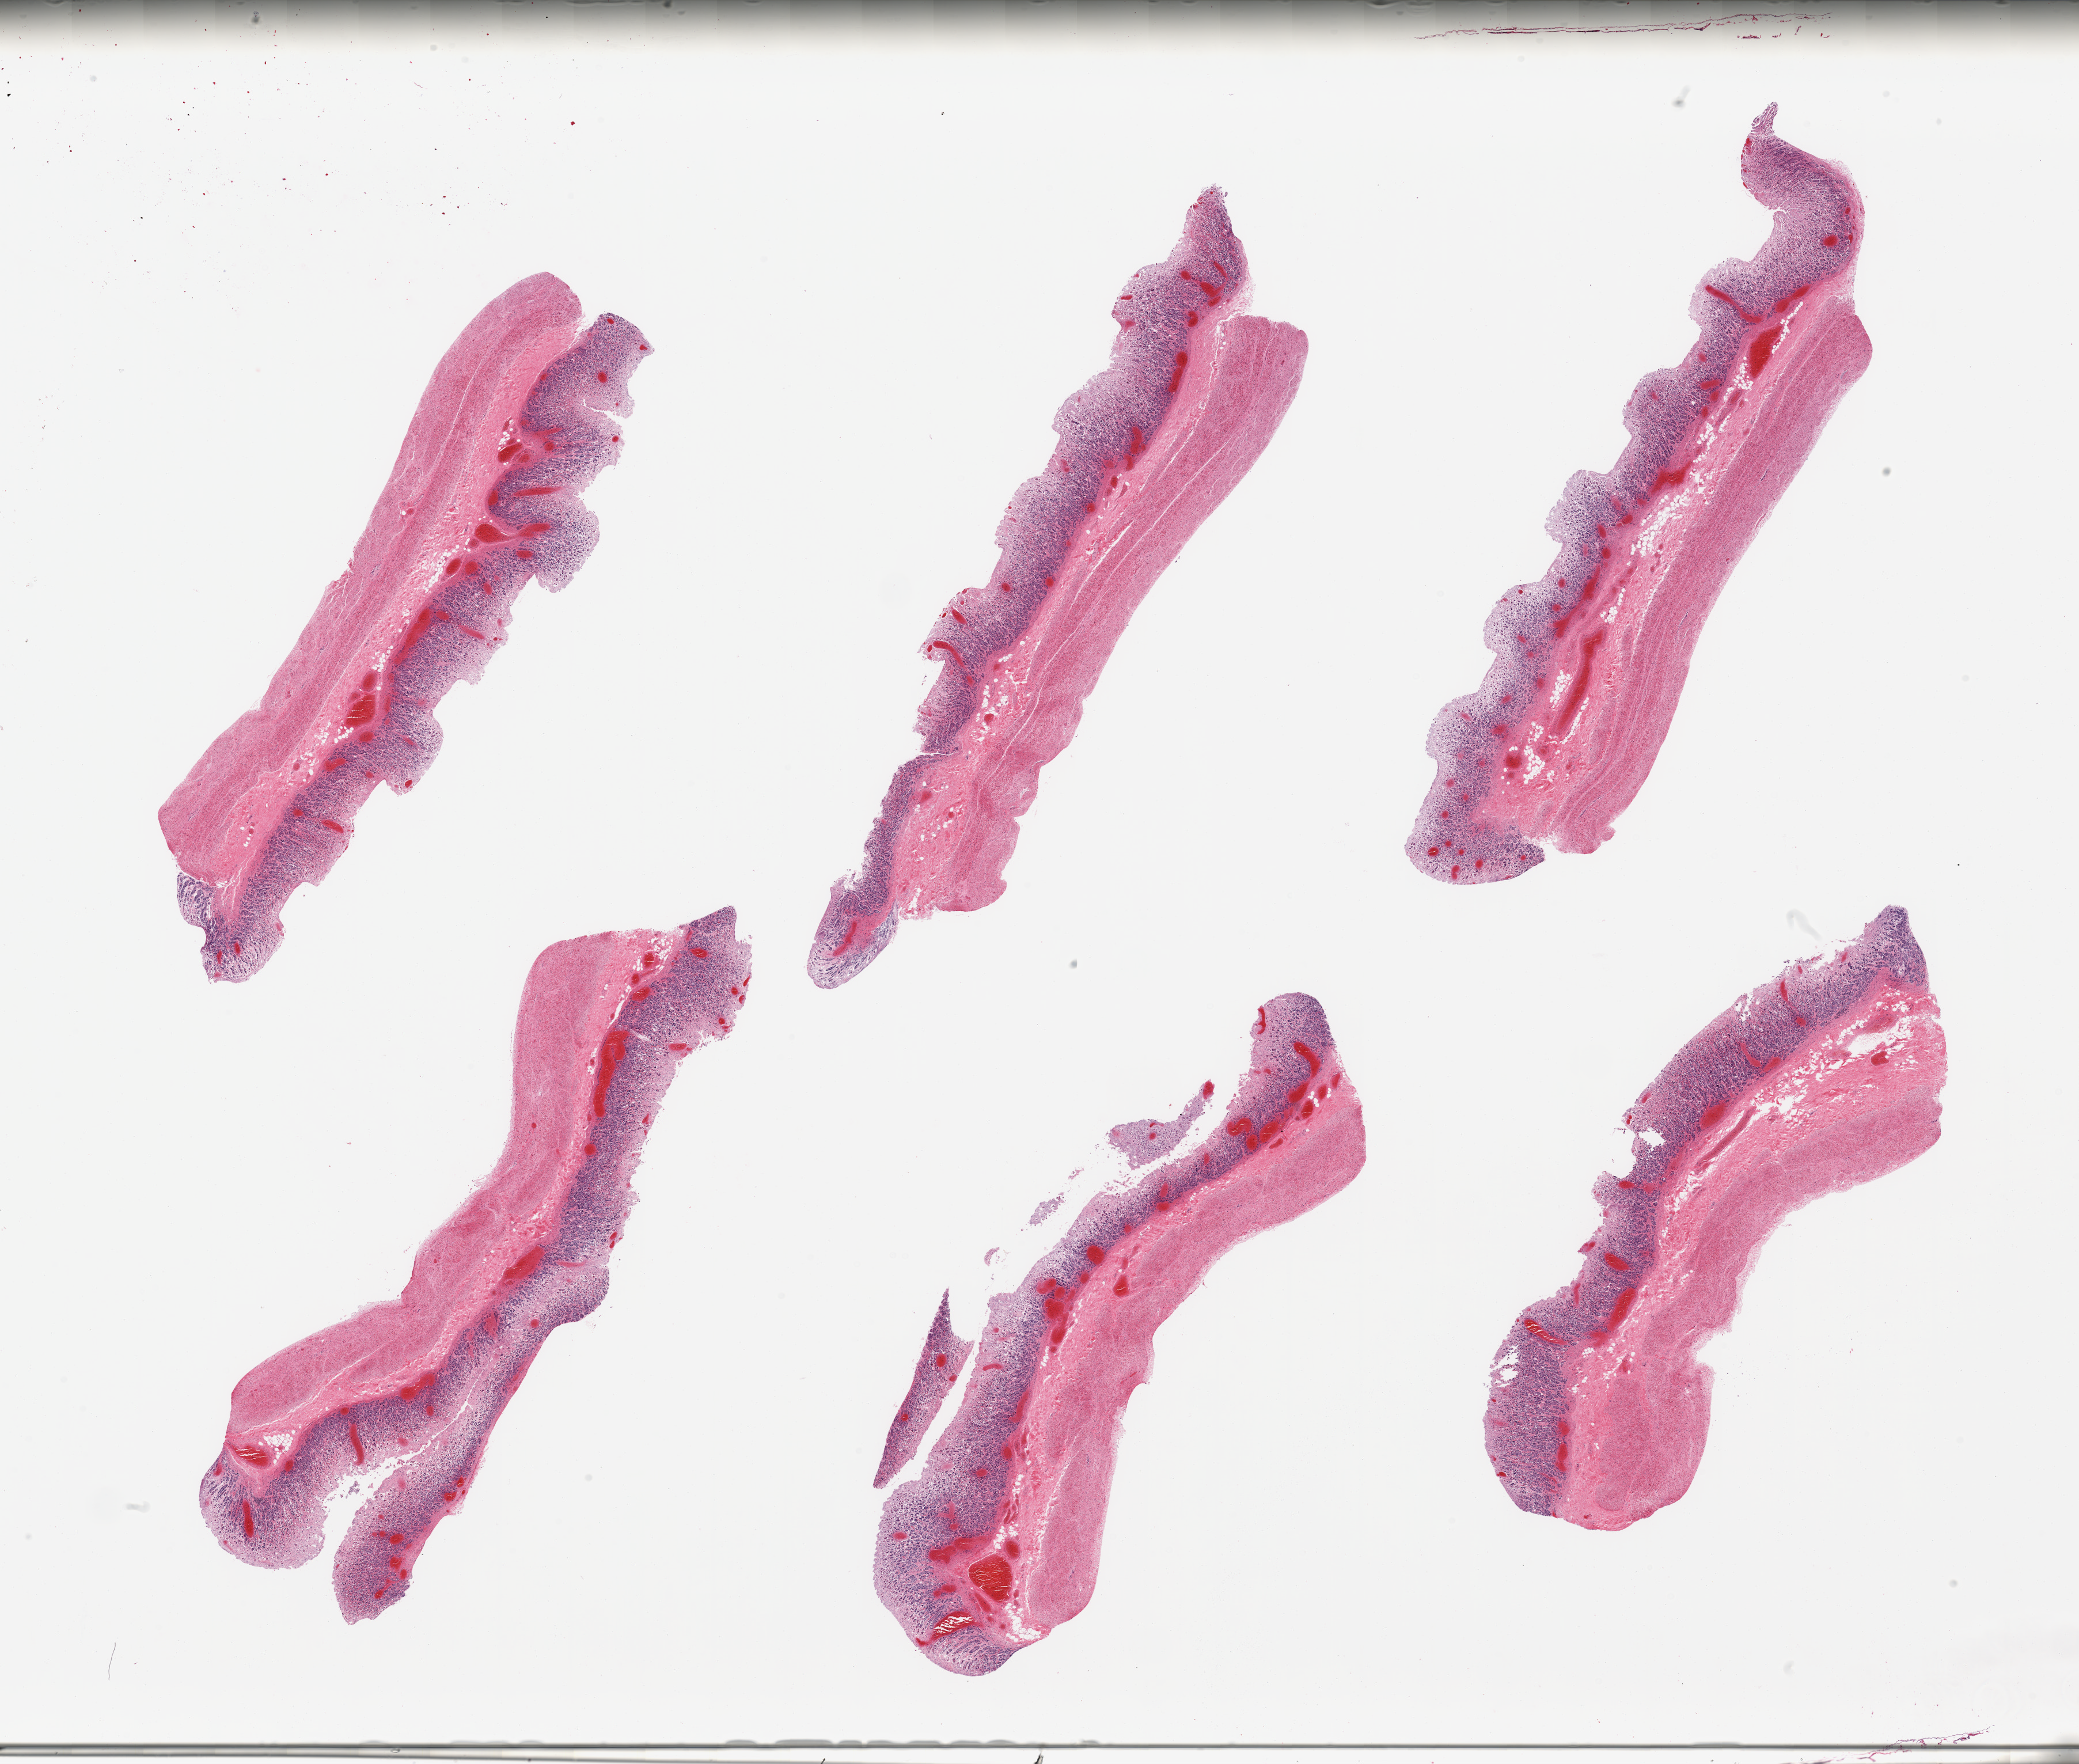
Whole-slide image, H&E stain — low-resolution overview of the scanned area, about 28.5 x 24.2 mm, PAXgene-fixed, paraffin-embedded tissue, target tissue: stomach, tissue donor sample. Donor sex: male.
Review note (as recorded): 6 pieces; mucosa largely digested or autolyzed.